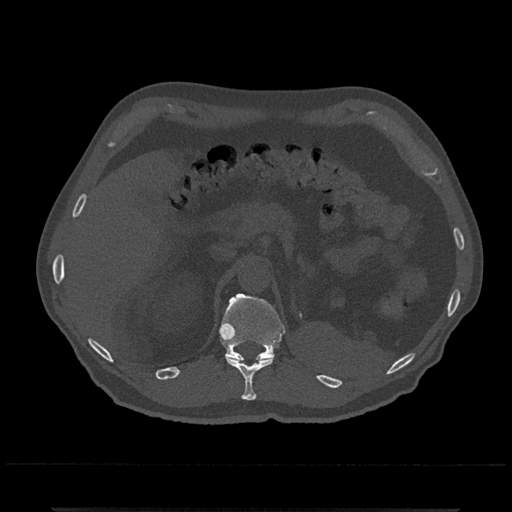
CT including the spine, one axial slice. Slice 458 of 797 in the series (ordered by position). Reconstruction kernel Br40s/3. 120 kVp. Bone window (W 1800 / L 400 HU). 0.5 mm slice thickness. 512 × 512 image matrix. Patient: male, 67 years. Case-level facts recorded for this patient, not image findings: primary cancer: prostate.
Annotated regions visible in this slice (semi-automatic segmentation, software-assisted and operator-edited):
- T11 vertebra: box from (x=225, y=356) to (x=274, y=401) px
- T12 vertebra: (x=219, y=293)–(x=286, y=361)